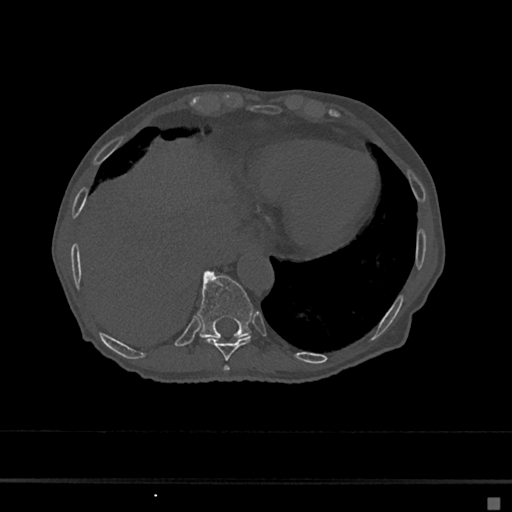
CT including the spine, one axial slice; position 248 of 797 along the scan axis; reconstruction kernel Br40s/3; bone window (W 1800 / L 400 HU); 0.5 mm slice thickness; 512 × 512 image matrix, field of view 360 × 360 mm. Patient: female, 68 years. Case-level facts recorded for this patient, not image findings: primary cancer: renal.
Outlined on this slice (semi-automatic segmentation, software-assisted and operator-edited):
- T10 vertebra: bounding box (x1, y1, x2, y2) in pixels: (197, 271, 253, 339)
- T8 vertebra: (224, 366, 229, 372)
- T9 vertebra: (204, 336, 252, 361)